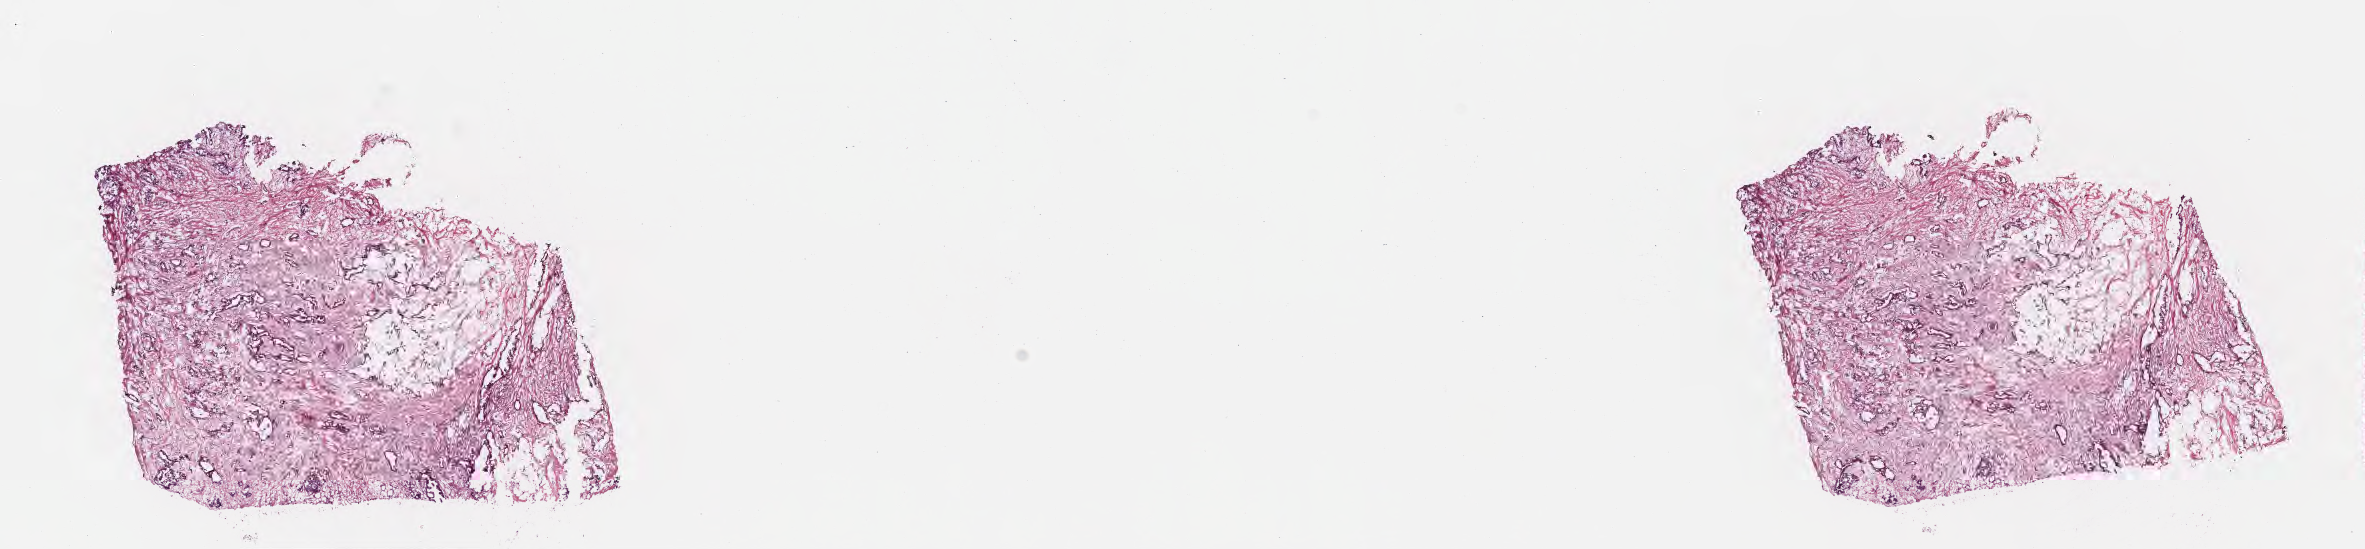
Digitized H&E-stained section — a low-resolution overview of the entire scanned area, about 19.1 x 4.4 mm, frozen section, specimen: primary tumor, anatomic site: head of pancreas. Female patient; age at initial diagnosis 60 years. Tumor grade: G3 (poorly differentiated). Pathologist review of this section (percent, as recorded): tumor cells 20%, tumor nuclei 20%, stromal cells 20%, necrosis 0%, normal cells 60%. Inflammatory infiltration, as recorded: lymphocyte infiltration 5%, monocyte infiltration 2%, neutrophil infiltration 5%.
AJCC pathologic stage: Stage III. Histologic diagnosis: Infiltrating duct carcinoma, NOS. Section: top of the tissue portion.